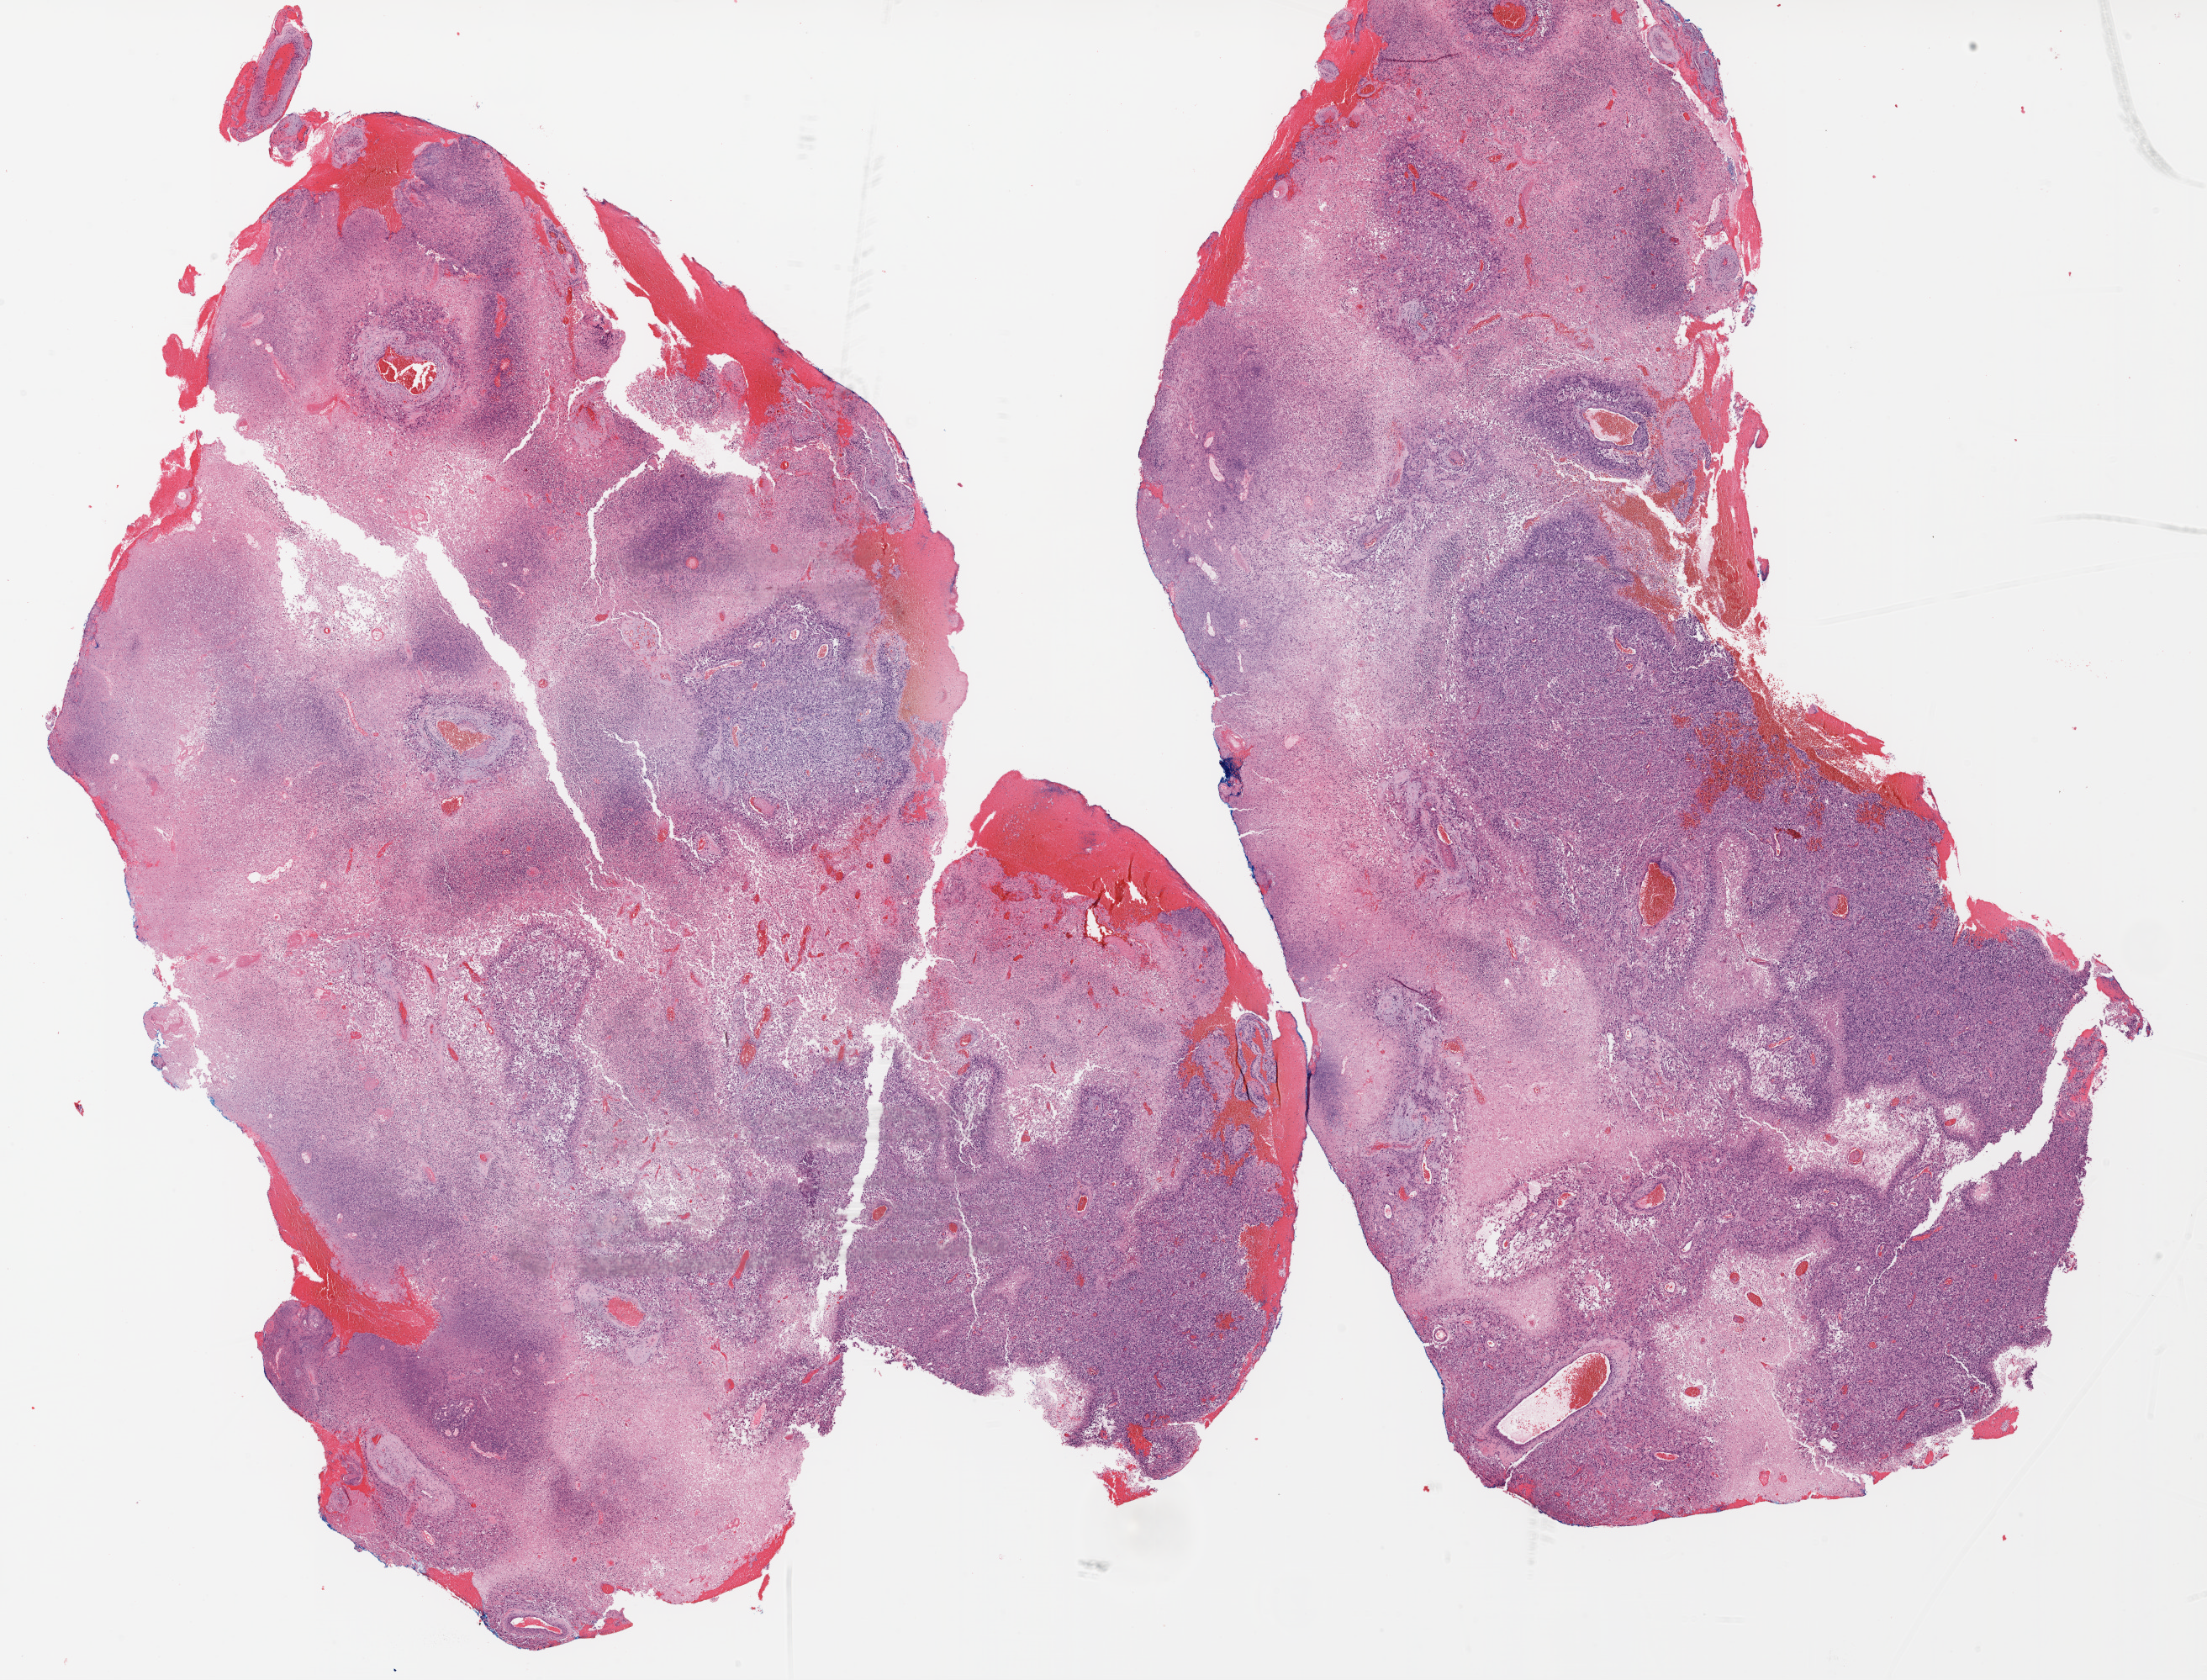
Digitized H&E tissue section (whole slide), shown as a low-resolution overview of the whole scanned area (about 21.1 x 16.0 mm). Formalin-fixed paraffin-embedded (FFPE) diagnostic section. Sample: primary tumour, brain. Male patient; age at initial diagnosis 66 years.
Pathologic diagnosis: Glioblastoma.